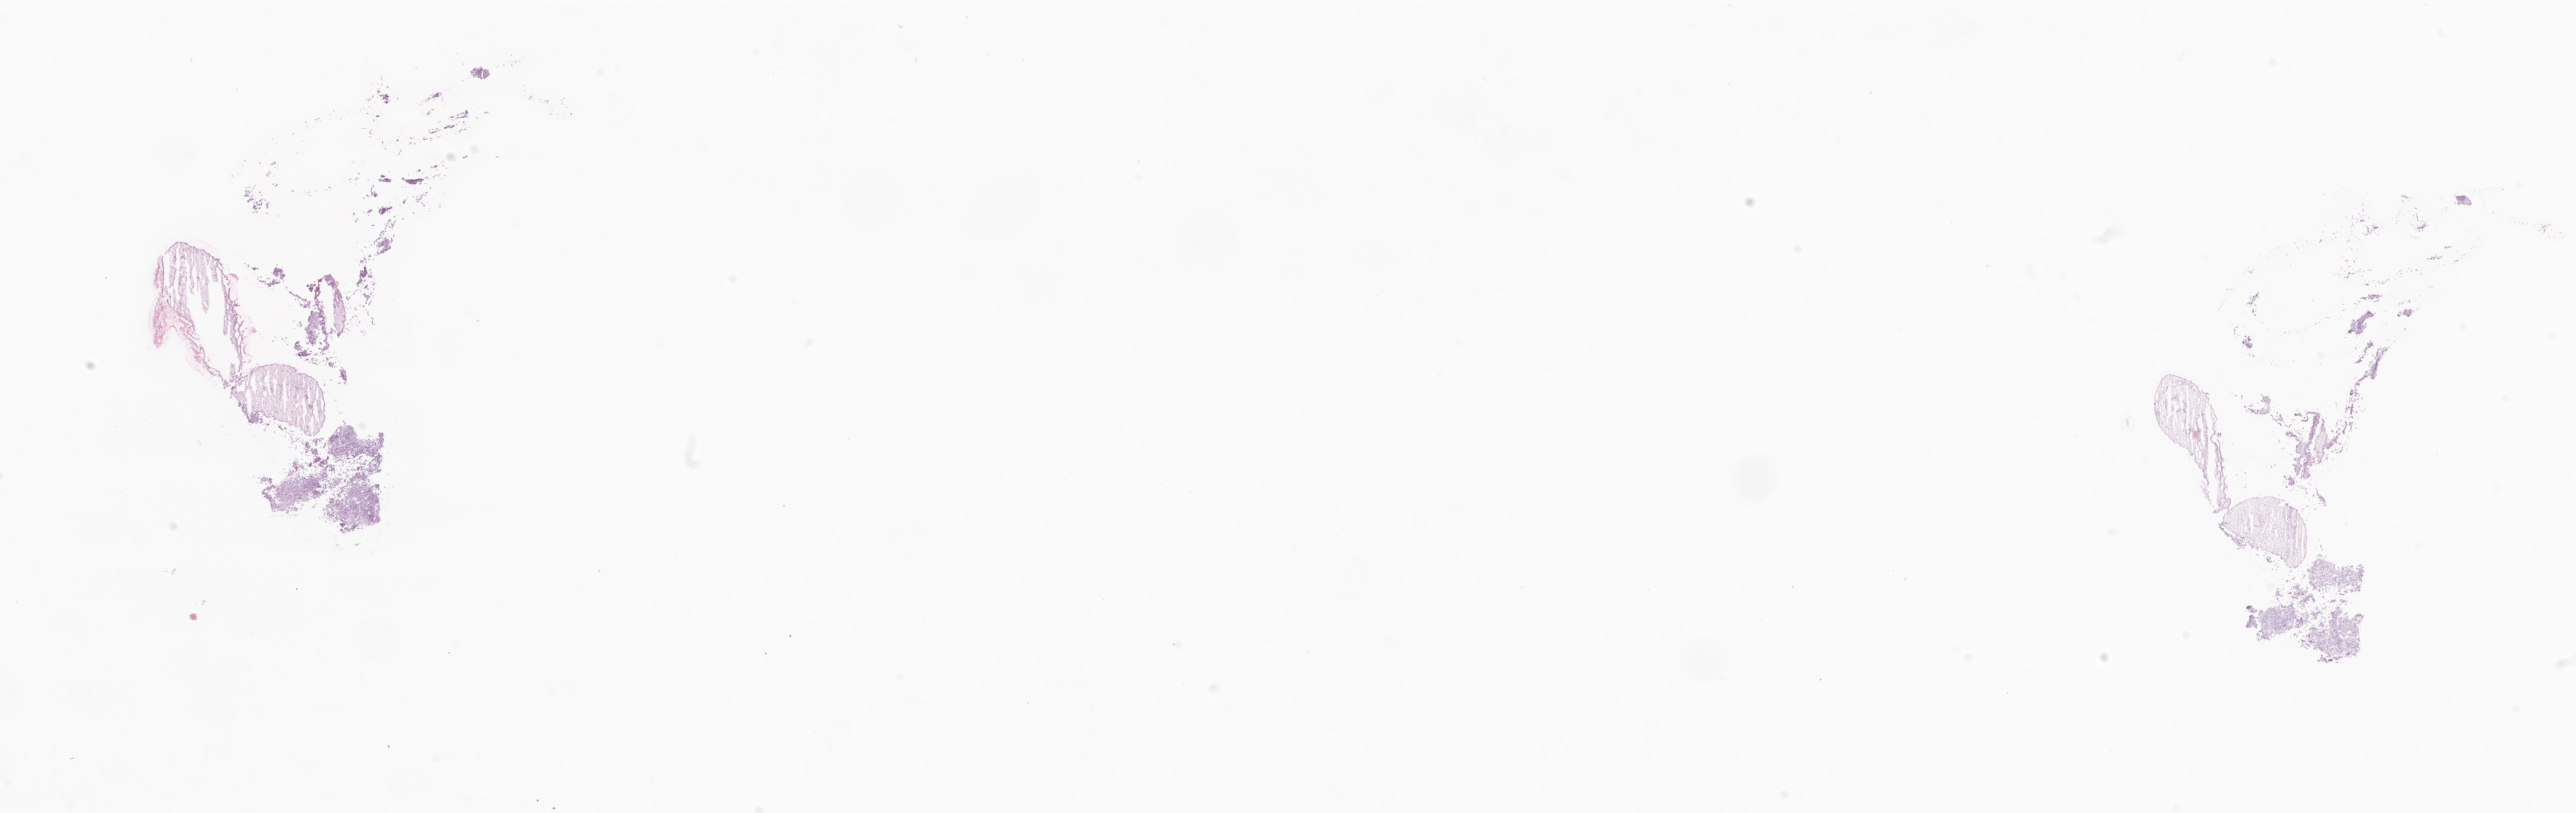
Hematoxylin and eosin (H&E) whole-slide image of tumor tissue from the brain — a low-resolution overview of the entire scanned area, about 31.5 x 9.9 mm; frozen section. Female patient, age 90 months (7 years 6 months).
* diagnosis (ICD-O-3 morphology term): Glioma, malignant